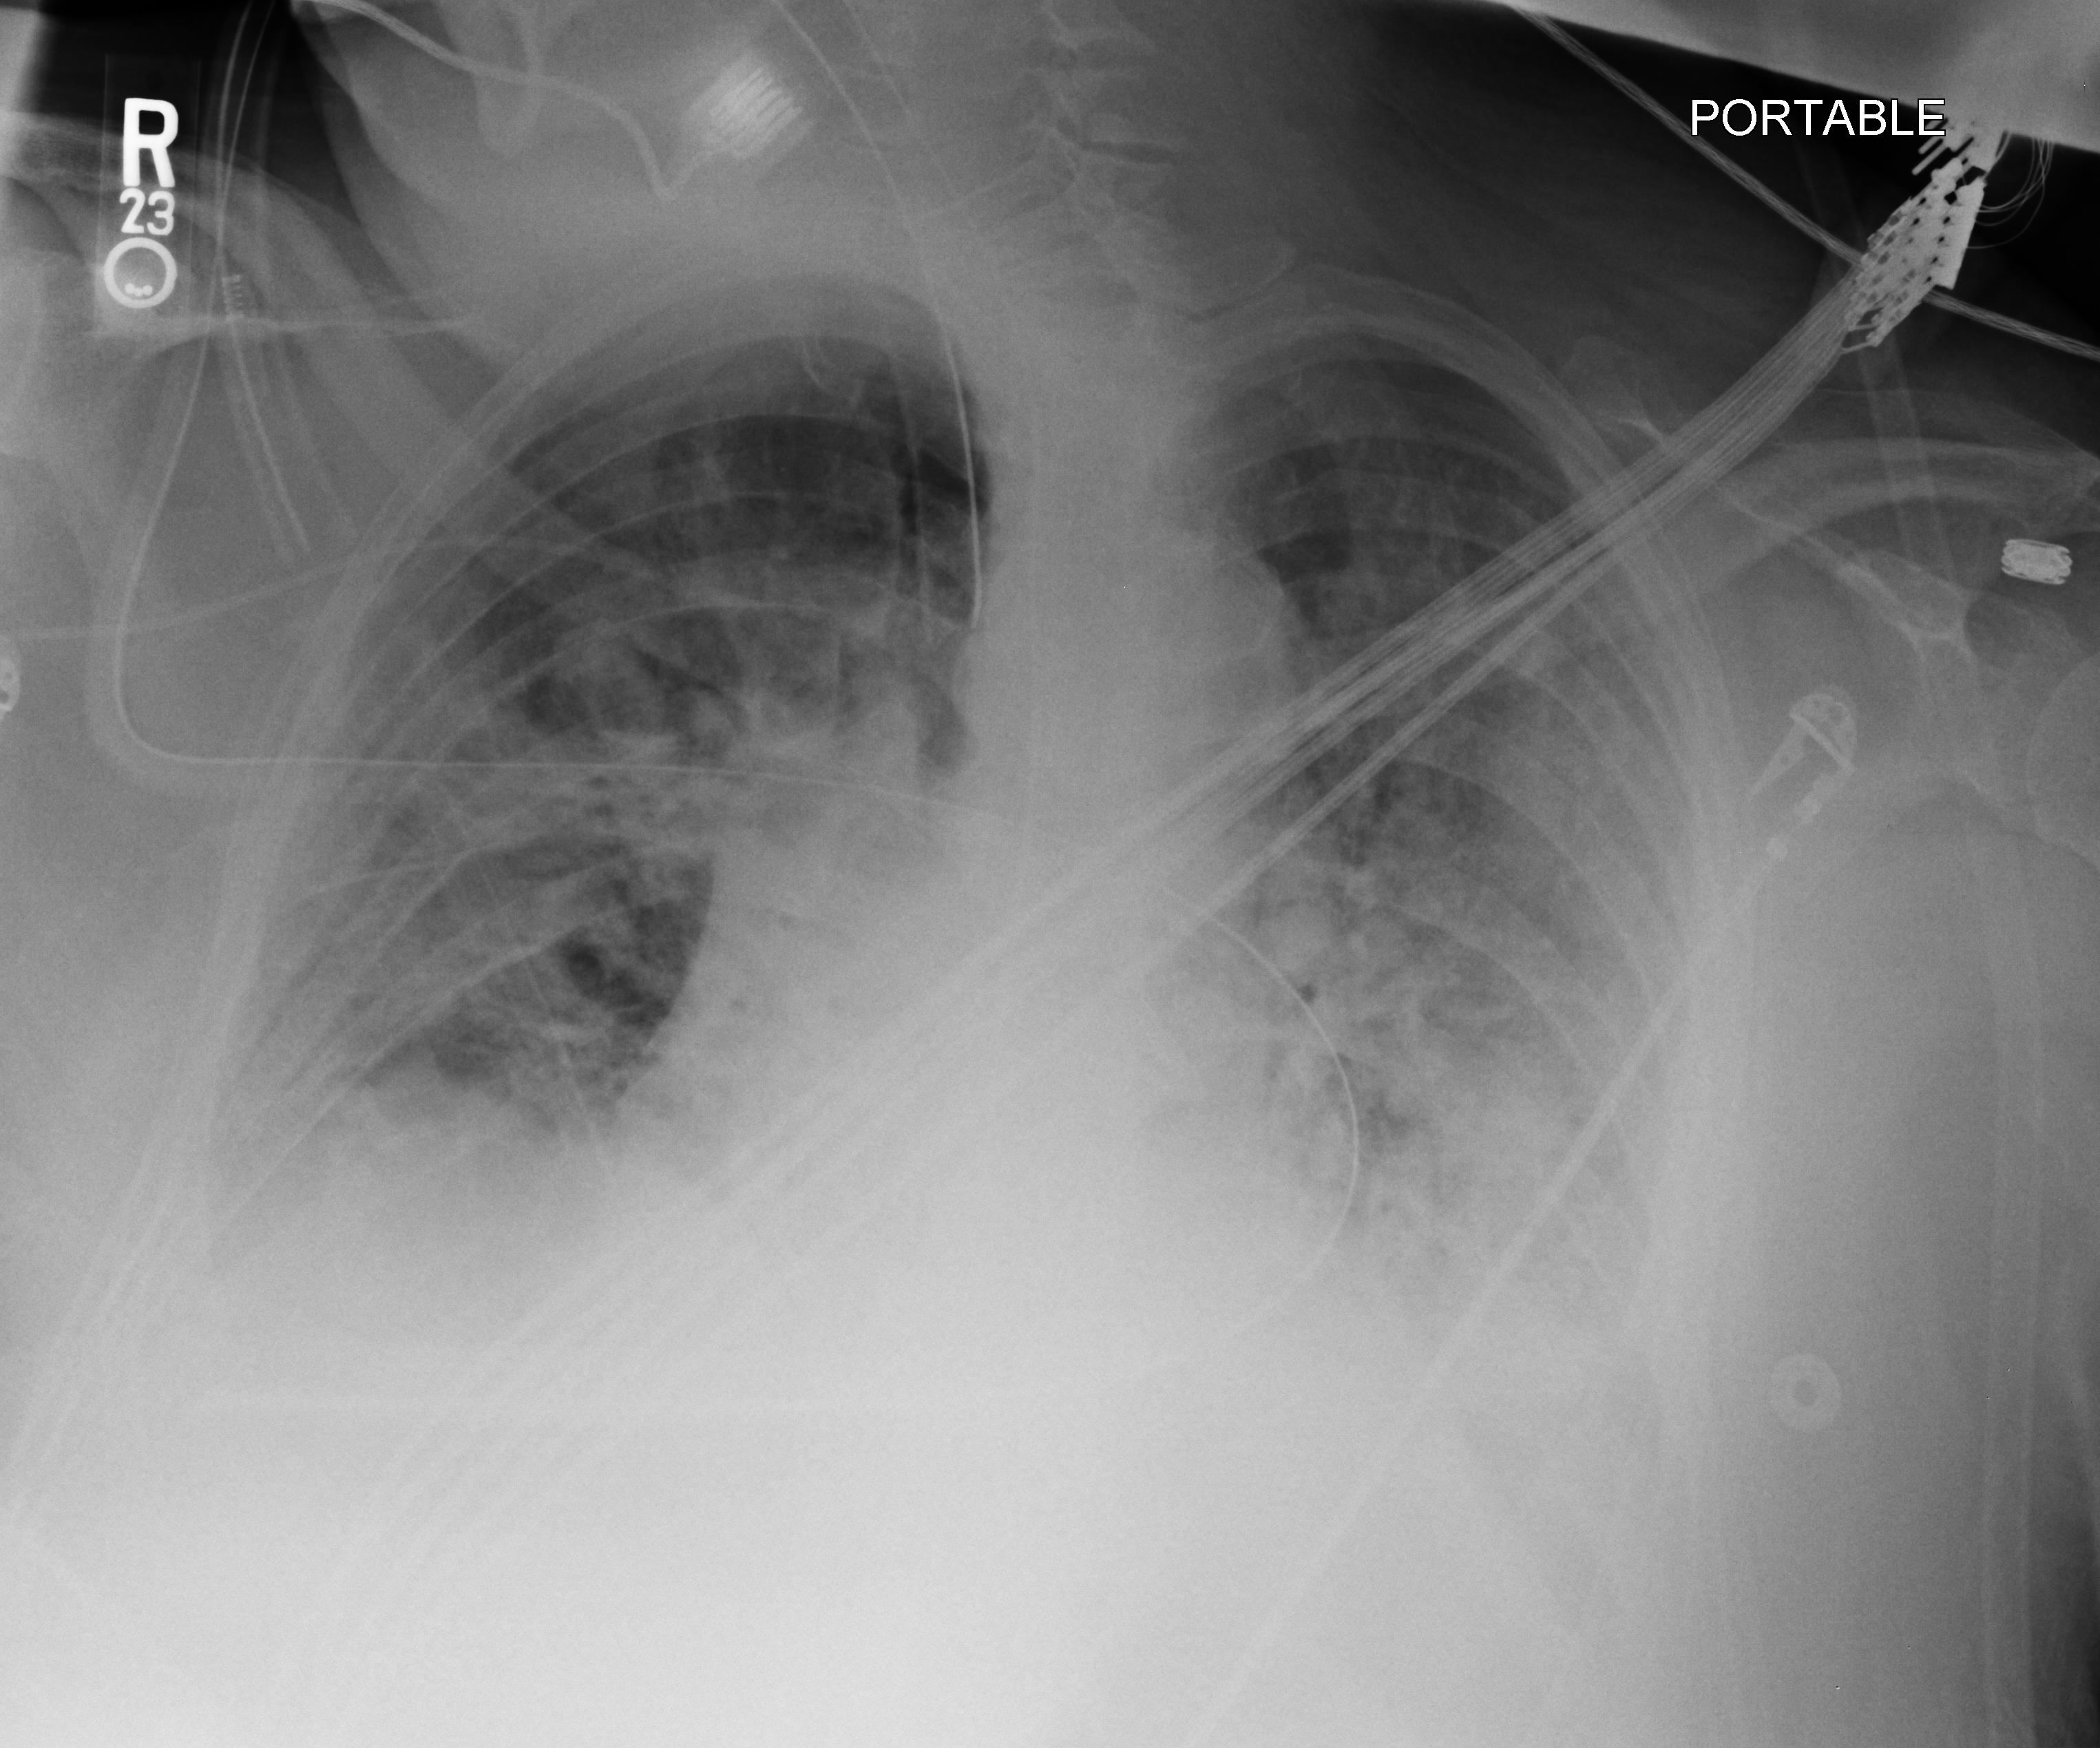
Chest X-ray (portable). Patient hospitalised with COVID-19; male, aged 60–74 years.
Admission-level facts for this patient (not findings on this image; timing relative to this image not recorded):
- admitted to intensive care during this hospital stay: yes
- mechanically ventilated during this hospital stay: yes